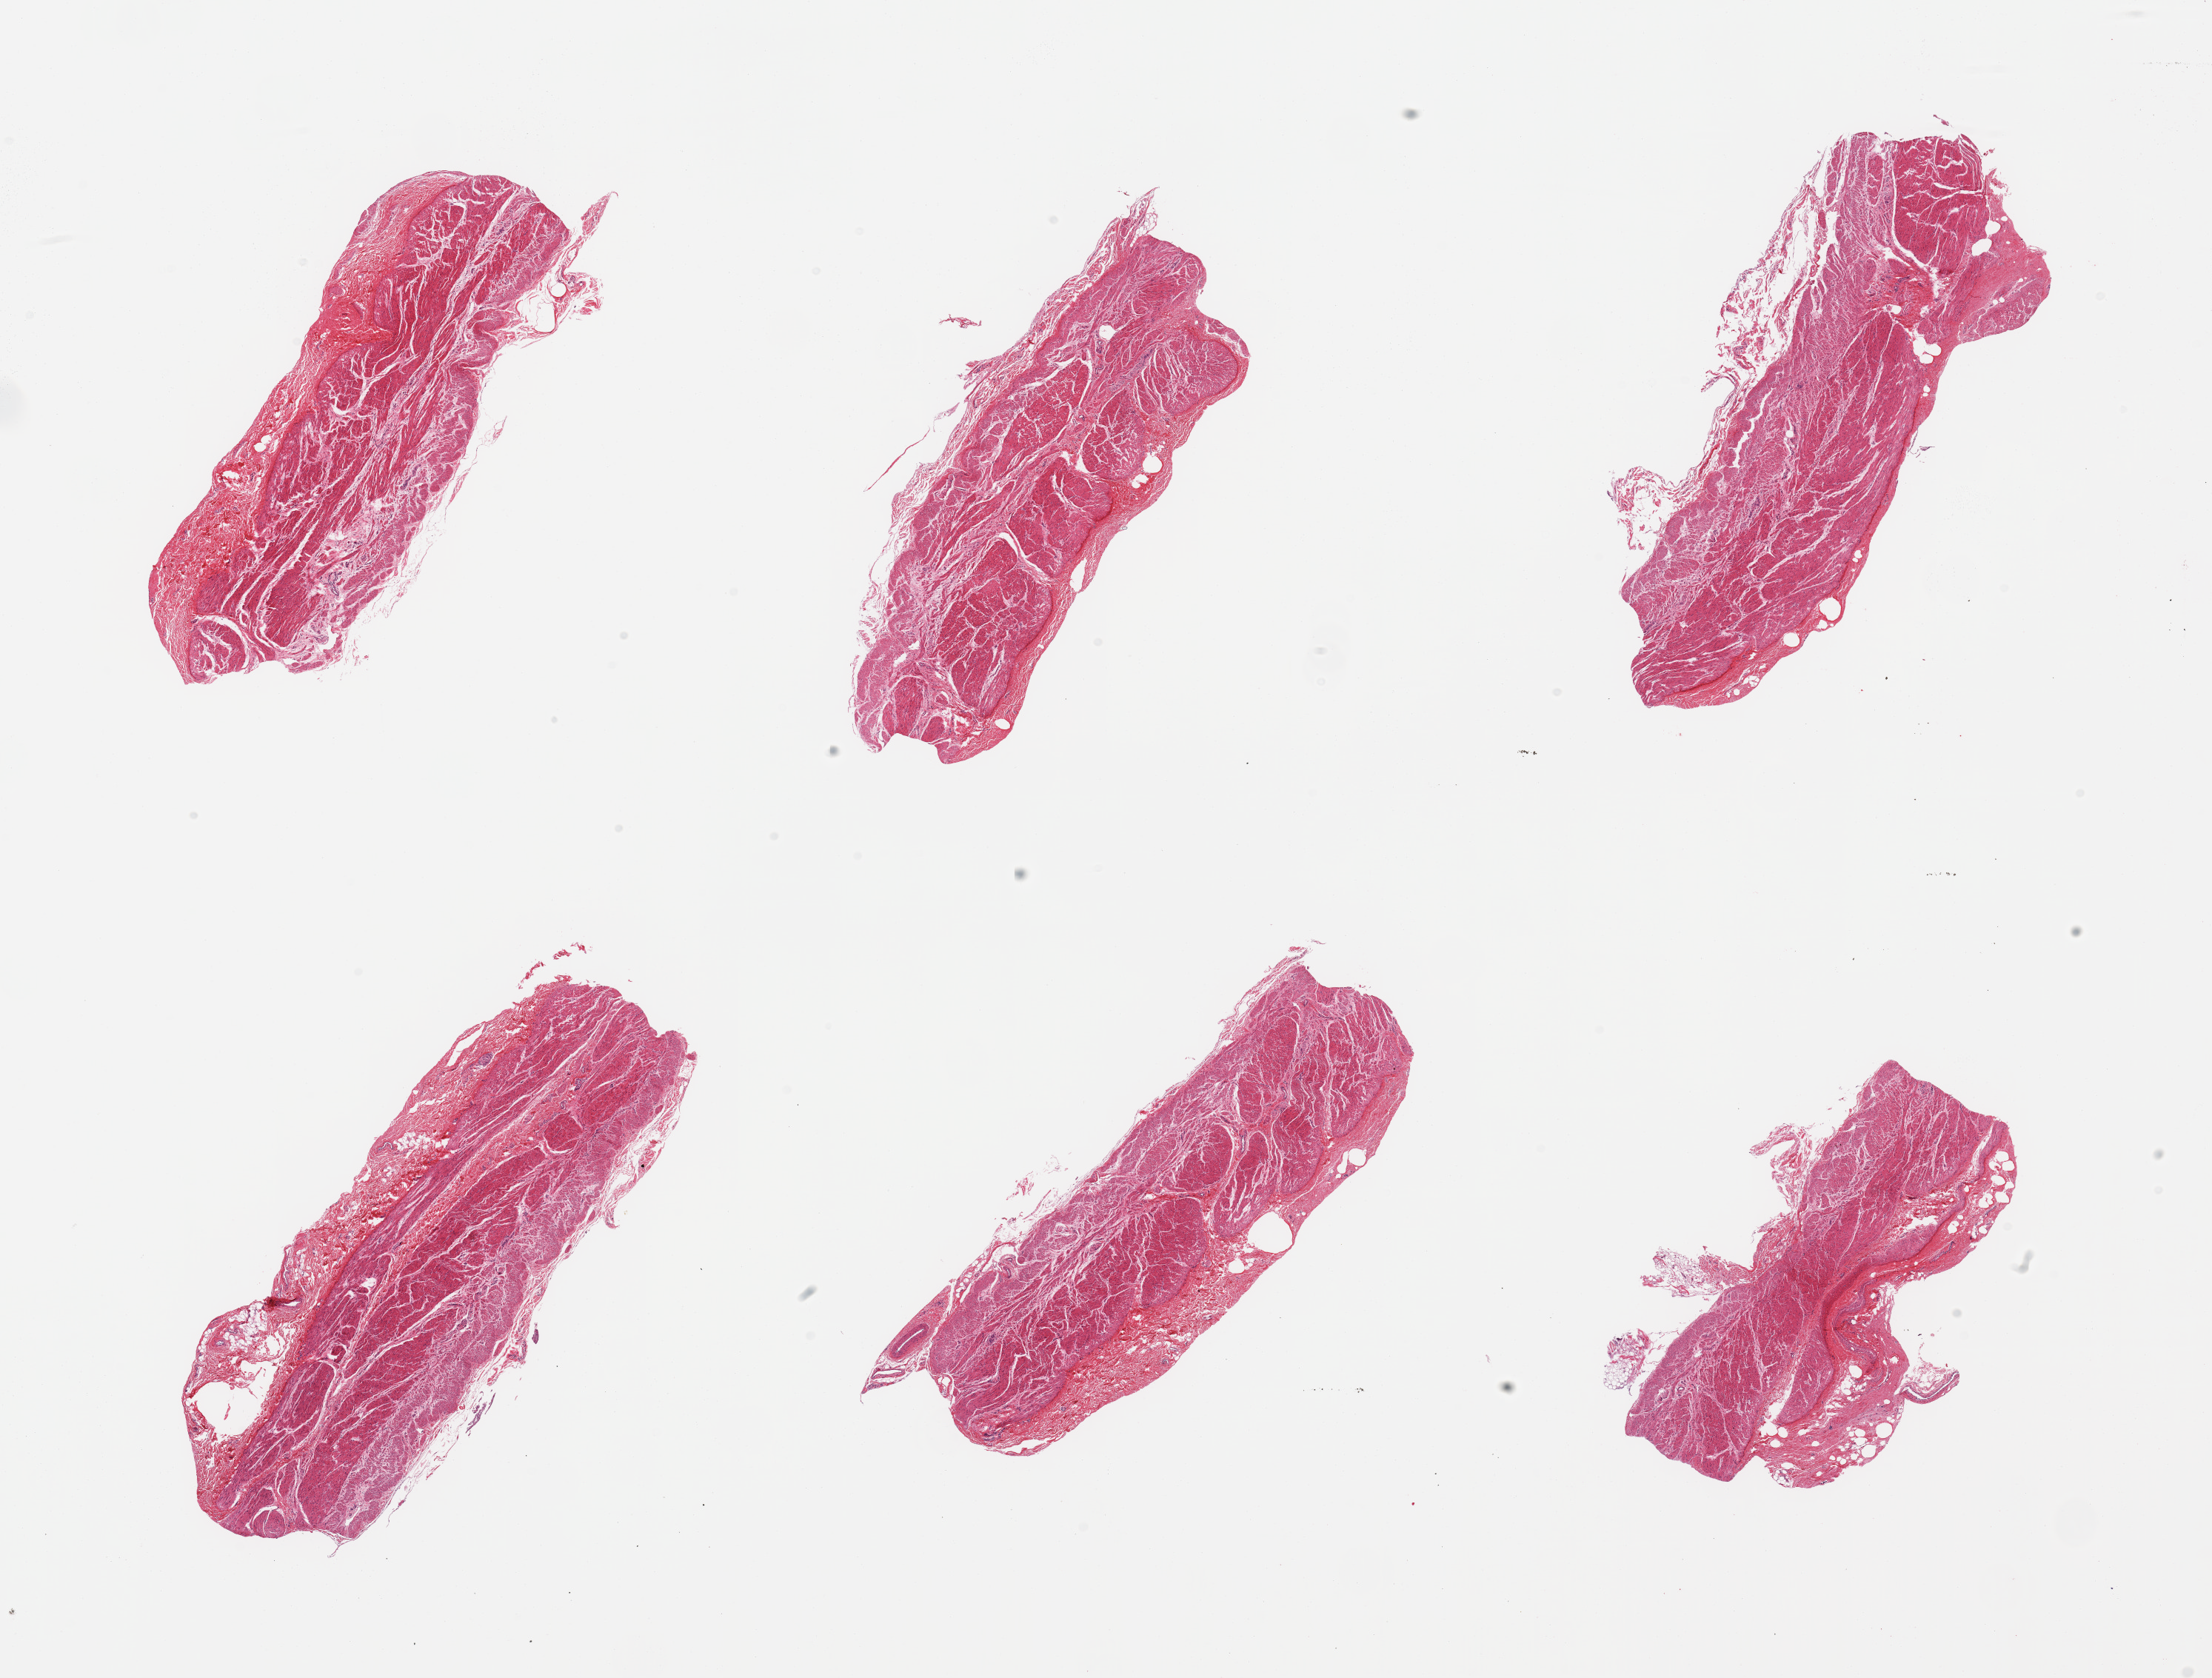
Whole-slide image, haematoxylin and eosin stain, brightfield — a low-resolution overview of the entire scanned area, about 23.6 x 17.9 mm; PAXgene-fixed paraffin-embedded (PFPE) section; sampled site (target tissue): stomach; tissue donor sample.
Review note (as recorded): 6 pieces, muscularis only, mucosa sloughed, presumed autolyzed.